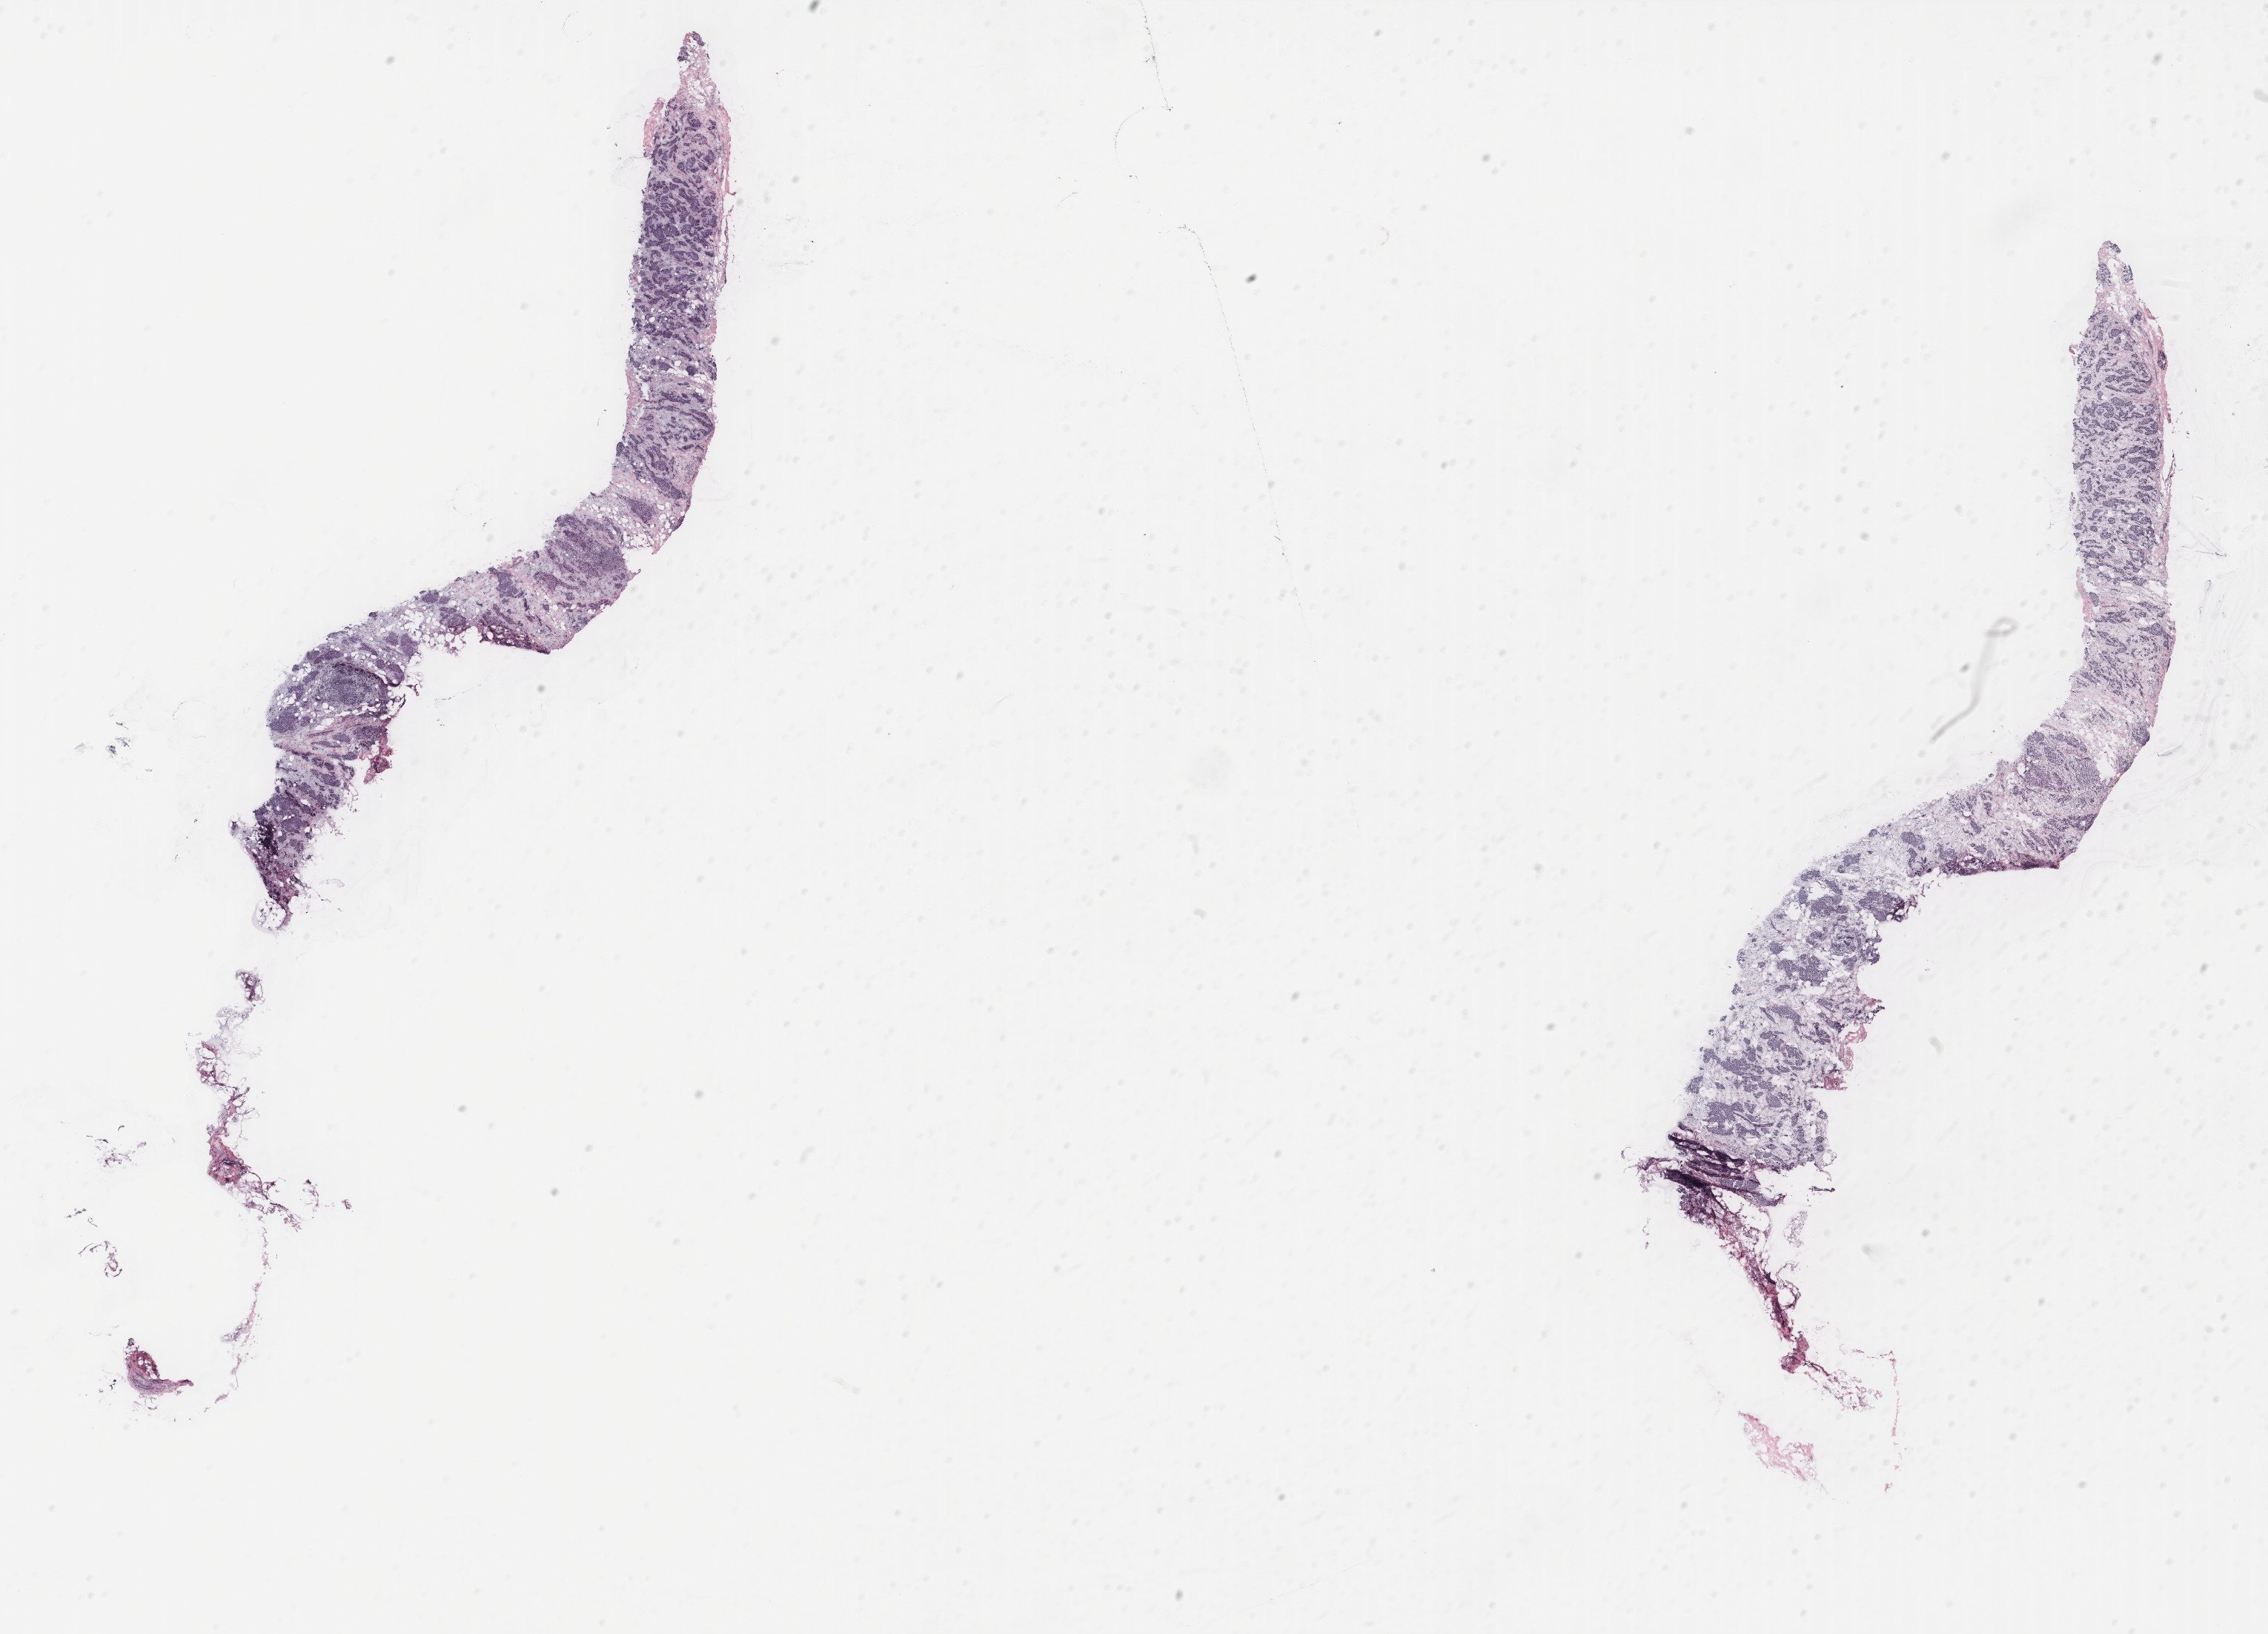
Whole-slide histology image, Hematoxylin and eosin (H&E) stained, shown as a low-resolution overview of the whole scanned area (about 24.5 x 17.6 mm); breast, tissue type not recorded.
• patient diagnosis (cohort enrolment): breast cancer (breast)